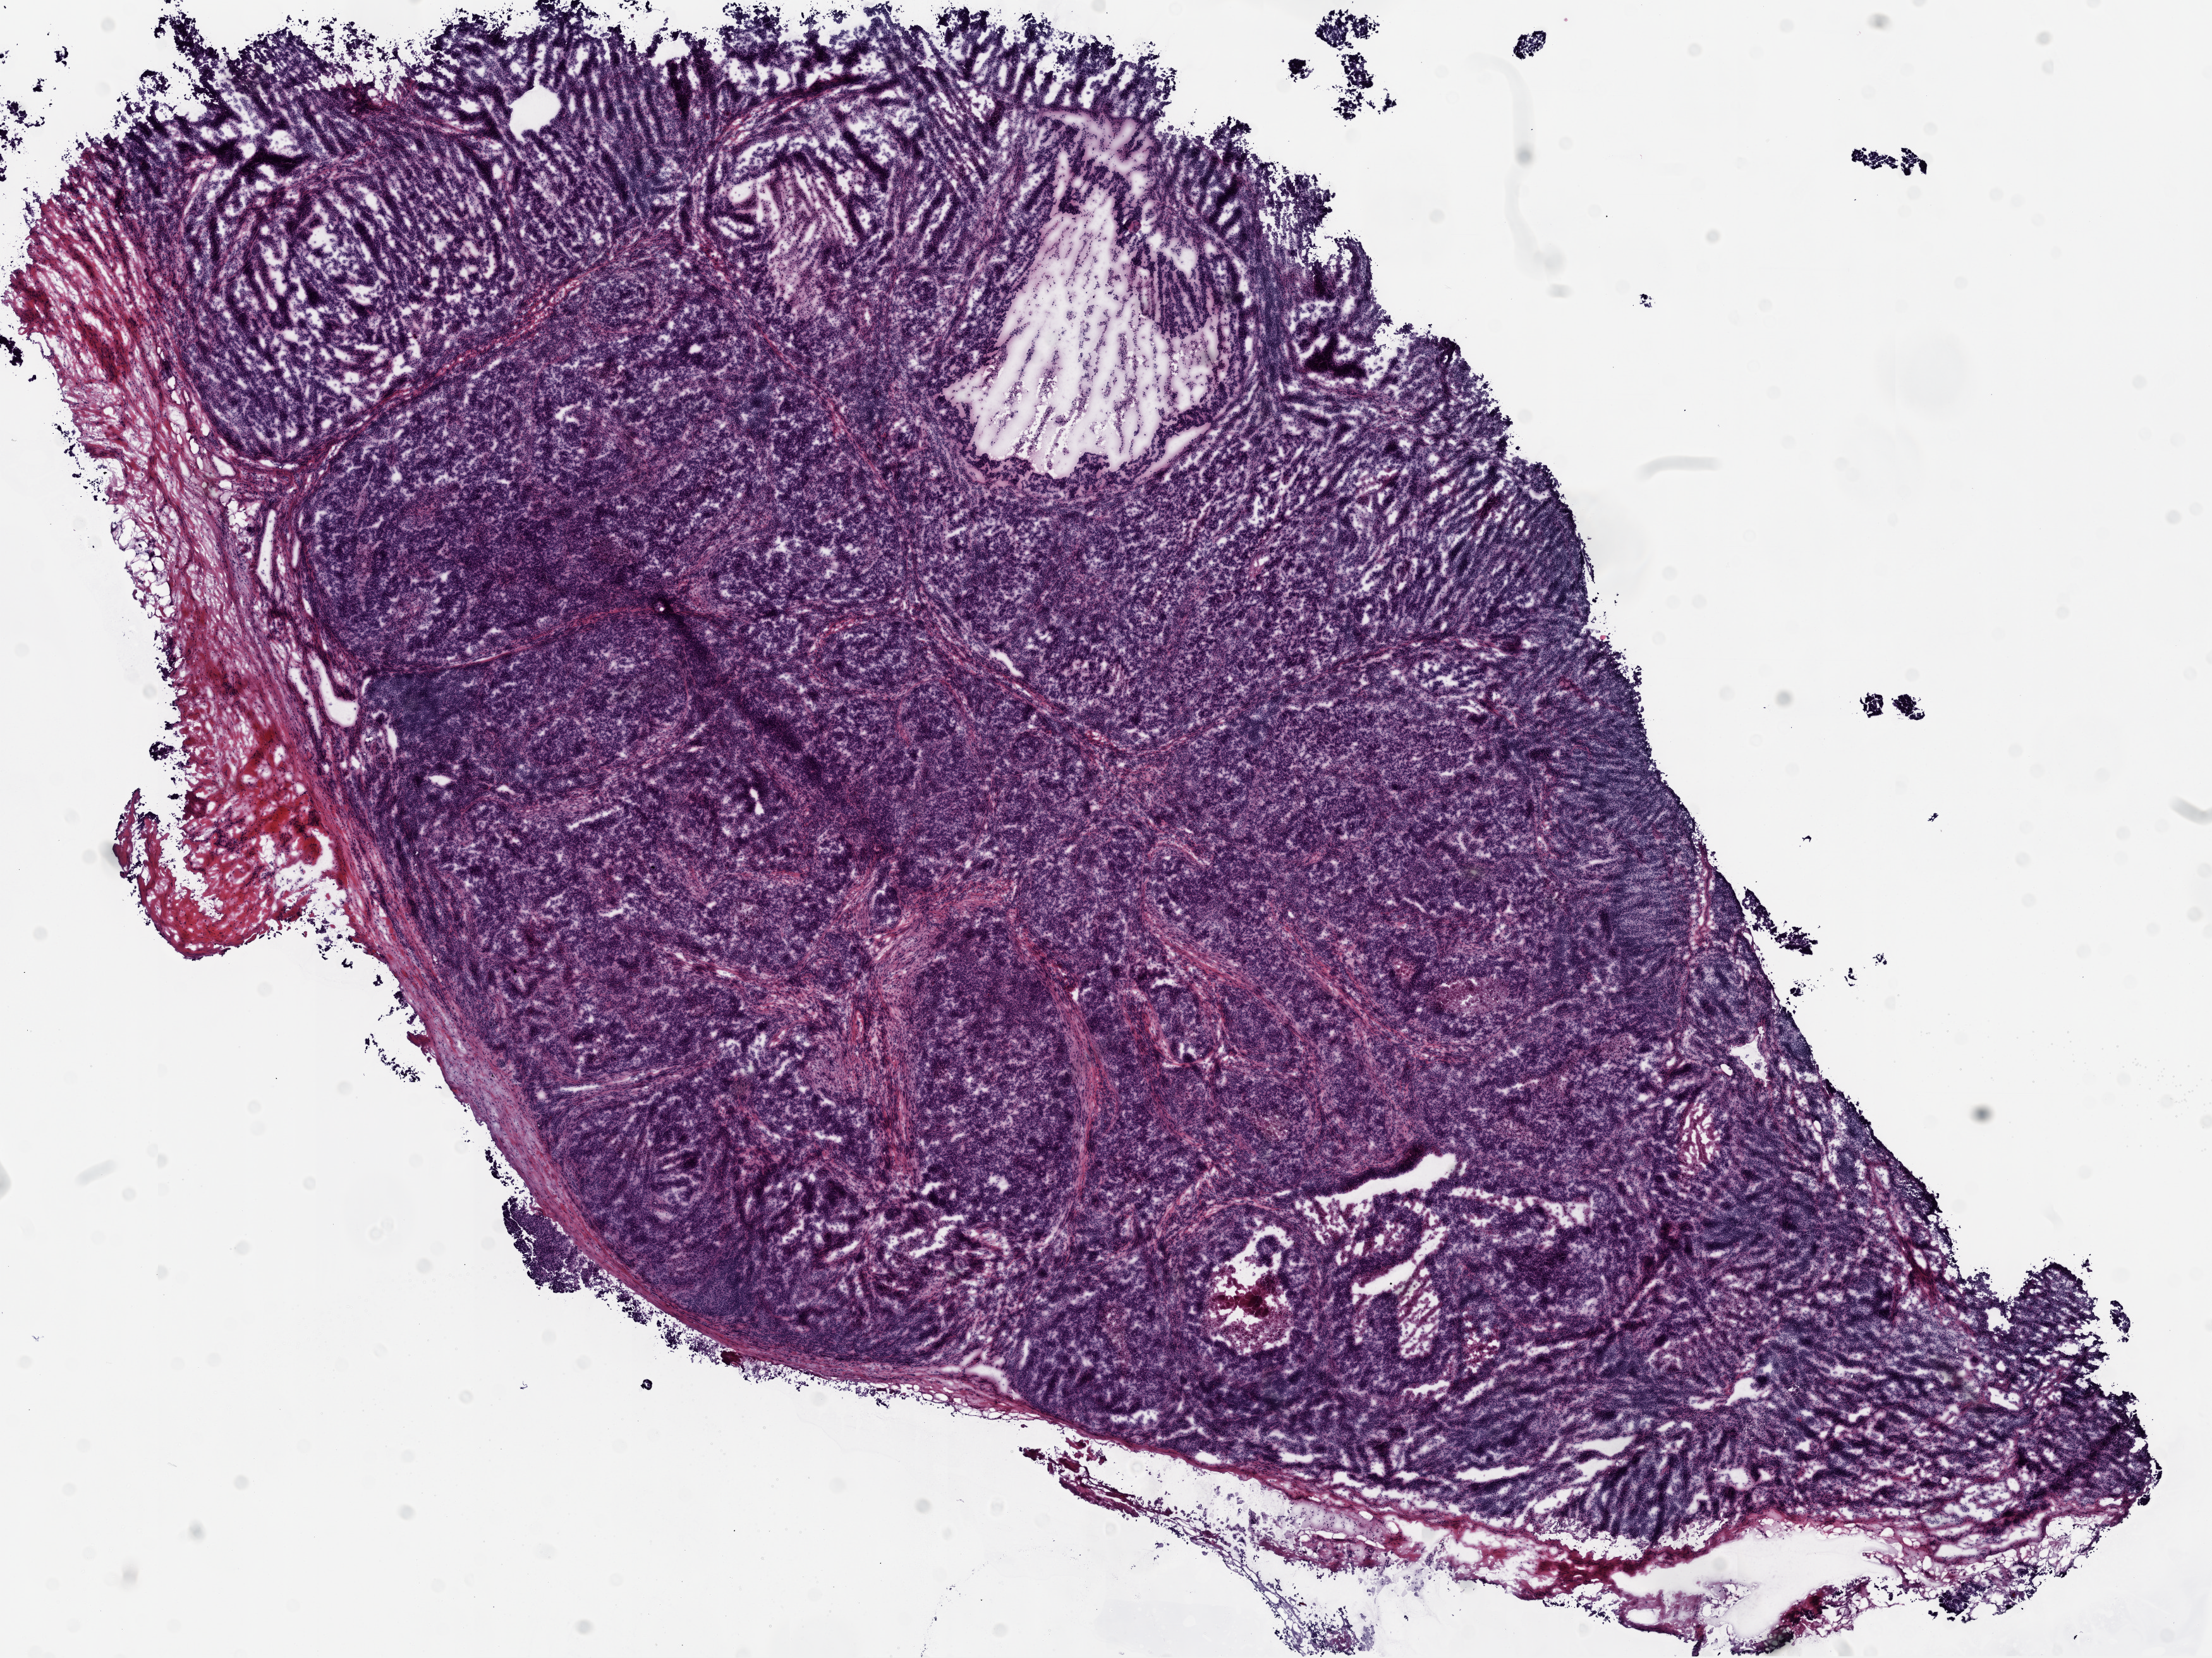
Digitized H&E-stained tissue section (whole slide), low-resolution overview of the scanned area, about 14.0 x 10.5 mm (acquisition: 20x scan). Frozen section from the top of the tissue portion. Ovary, primary tumour sample. Female, age 62 years at initial diagnosis. Histologic grade: G3 (poorly differentiated). Pathologist review of this section (percent, as recorded): tumour cells 95%, tumour nuclei 98%, normal cells 0%, stromal cells 3%, necrosis 2%. Infiltration values recorded for this section: lymphocyte infiltration 60%, monocyte infiltration 10%, neutrophil infiltration 20%.
Diagnosis: Serous cystadenocarcinoma, NOS. FIGO stage: IIIC.